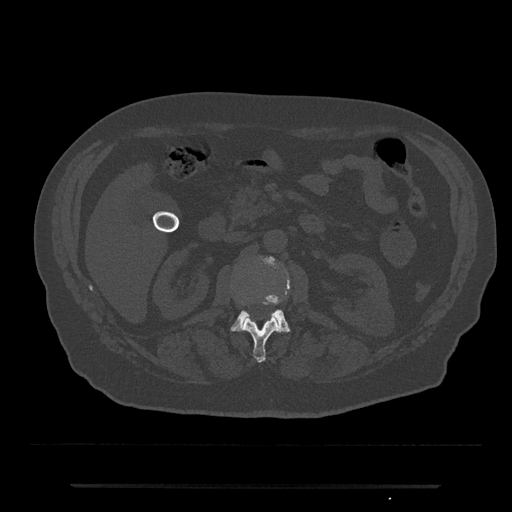
CT including the spine, one axial slice; position 505 of 797 along the scan axis; reconstruction kernel Br40s/3; 120 kVp; bone window (W 1800 / L 400 HU); 0.5 mm slice thickness; 512 × 512 image matrix, field of view 434 × 434 mm. Male patient, age 80 years. From the clinical record (not read from this slice): primary cancer: prostate.
Outlined on this slice (semi-automatically segmented with operator editing):
- L1 vertebra: bounding box (x1, y1, x2, y2) in pixels: (243, 317, 280, 363)
- L2 vertebra: (230, 256, 291, 333)